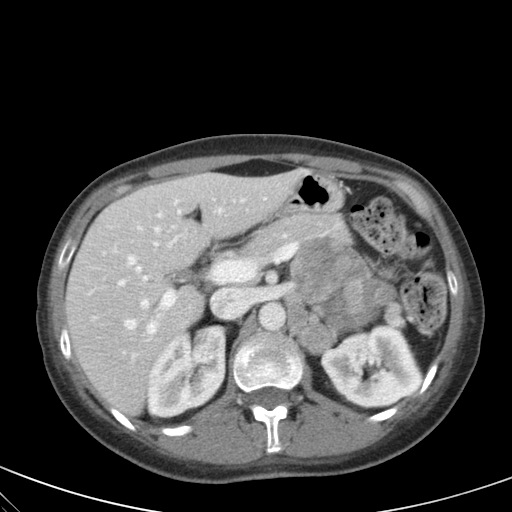
Contrast-enhanced abdominal CT, one axial slice; position 34 of 59 along the scan axis; intravenous contrast given; soft-tissue window (W 400 / L 40 HU); 4 mm slice thickness; 512 × 512 image matrix. Female patient, age 28 years. Case-level facts recorded for this patient, not image findings: diagnosis: adrenocortical carcinoma; tumour side: left adrenal; tumour size at pathology: 7 cm; Ki-67 index: 40 %; stage (as recorded): 4.
Annotated regions visible in this slice (semi-automatic segmentation, software-assisted and operator-edited):
- mass: bounding box <292,238,394,332> (left, top, right, bottom; pixels)